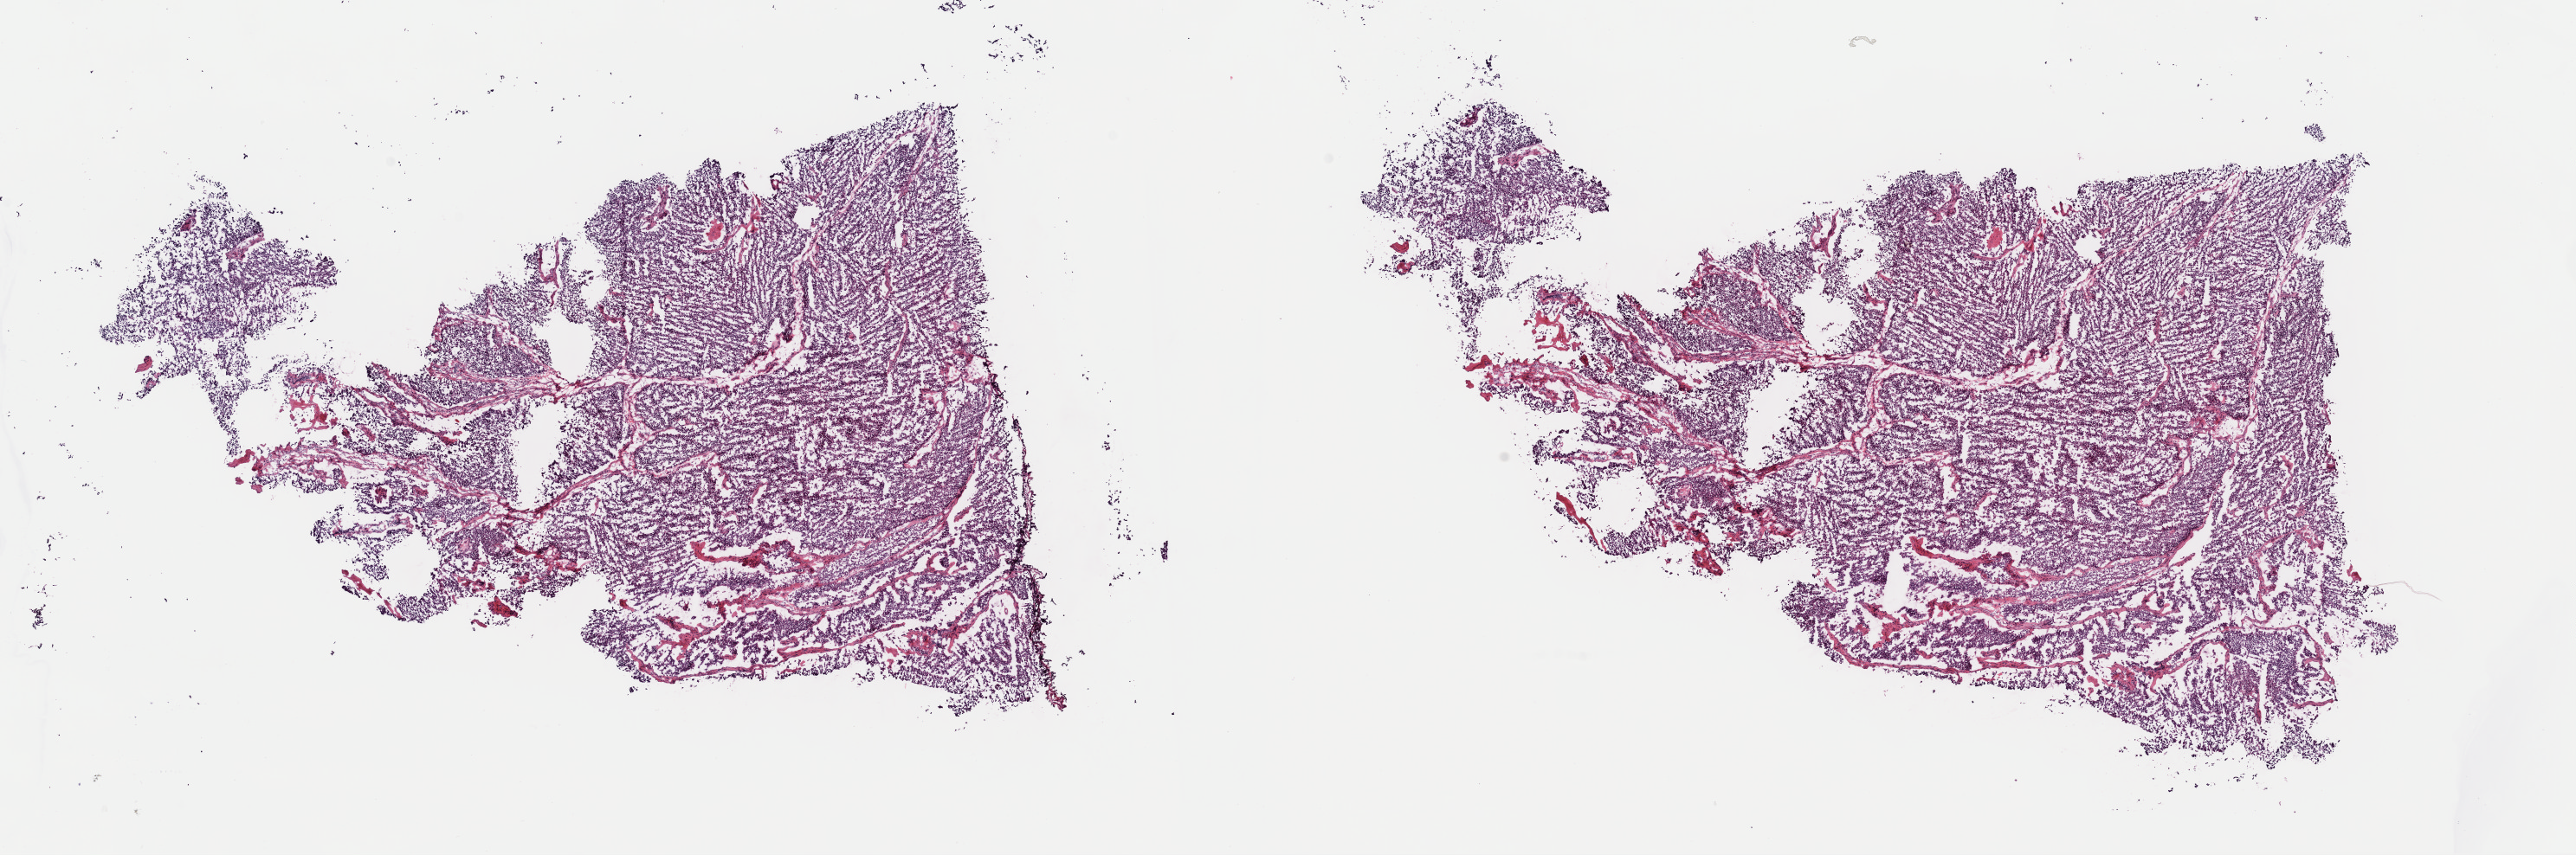
Digitized H&E tissue section (whole slide) — whole scanned area (about 23.5 x 7.8 mm) shown as a low-resolution overview. Frozen section from the top of the tissue portion. Bladder, primary tumour sample. Male, age 73 years at initial diagnosis. Histologic grade: low grade. Pathologist review of this section (percent, as recorded): tumour cells 68%, tumour nuclei 95%, normal cells 0%, stromal cells 20%, necrosis 12%. Infiltration values recorded for this section: lymphocyte infiltration 3%, monocyte infiltration 0%, neutrophil infiltration 0%.
- lymph nodes positive (case pathology): 0 of 14 examined
- pathologic diagnosis: Transitional cell carcinoma (trigone of bladder)
- AJCC pathologic stage: III (7th edition)
- TNM: T3 N0 M0